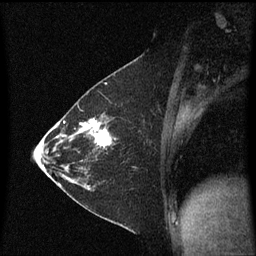
Breast MRI (dynamic contrast-enhanced), one sagittal slice; position 32 of 60 along the scan axis; dynamic contrast-enhanced series, image 2 of 3 at this slice position (ordered by acquisition); 1.5 T; TE 4.2 ms, TR 8.4 ms; 2 mm slice thickness; 256 × 256 image matrix. Patient: female, 36 years. From the clinical record (not read from this slice): setting: breast cancer imaged before/during neoadjuvant chemotherapy; receptor status: HR-positive, HER2-negative.
Annotated regions visible in this slice (semi-automatic segmentation, software-assisted and operator-edited):
- analysis volume of interest (the breast-tissue region the enhancement analysis was run in; not a lesion): bounding box (x1, y1, x2, y2) in pixels: (72, 116, 123, 187)
- tumour enhancement mask (voxels above the 70 % enhancement threshold inside the analysis volume of interest): (72, 120, 113, 149)